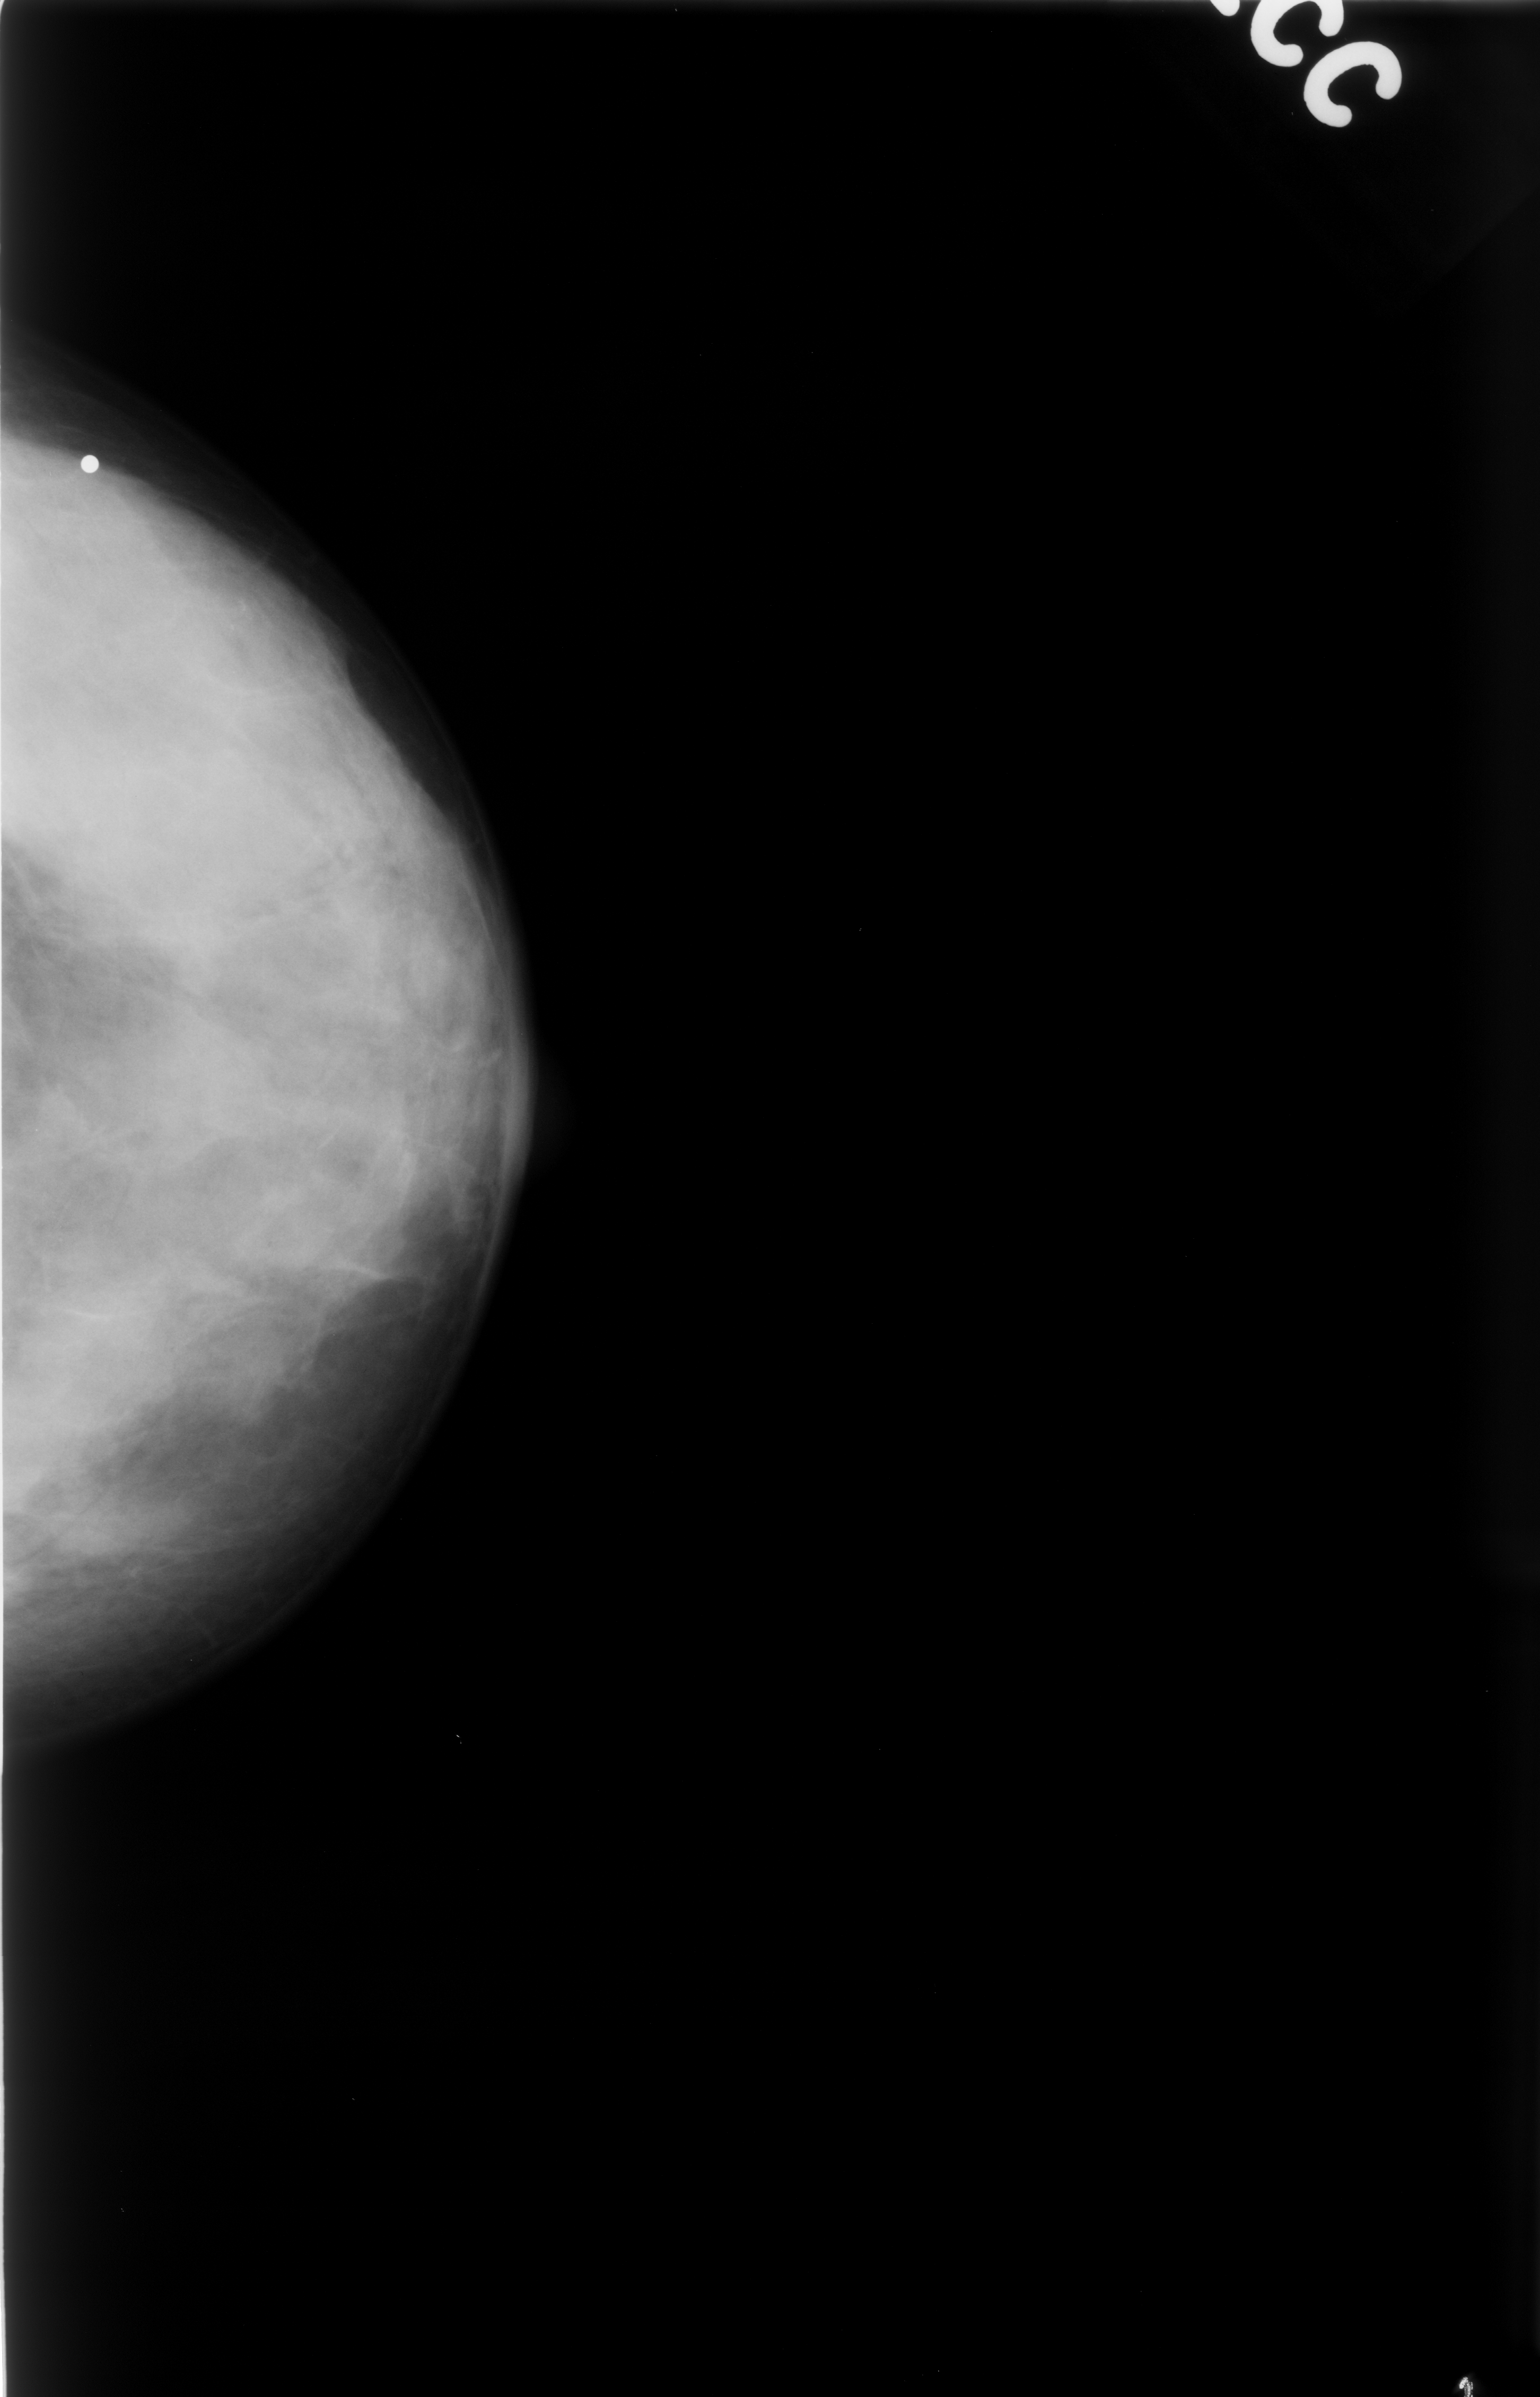
Scanned film-screen mammogram; left breast; craniocaudal (CC) view; breast composition: extremely dense (BI-RADS density category 4 of 4).
Calcifications, morphology amorphous, distribution clustered; BI-RADS assessment category 4; subtlety rating 3 on a 1 (subtle) to 5 (obvious) scale; pathology (as recorded): benign.